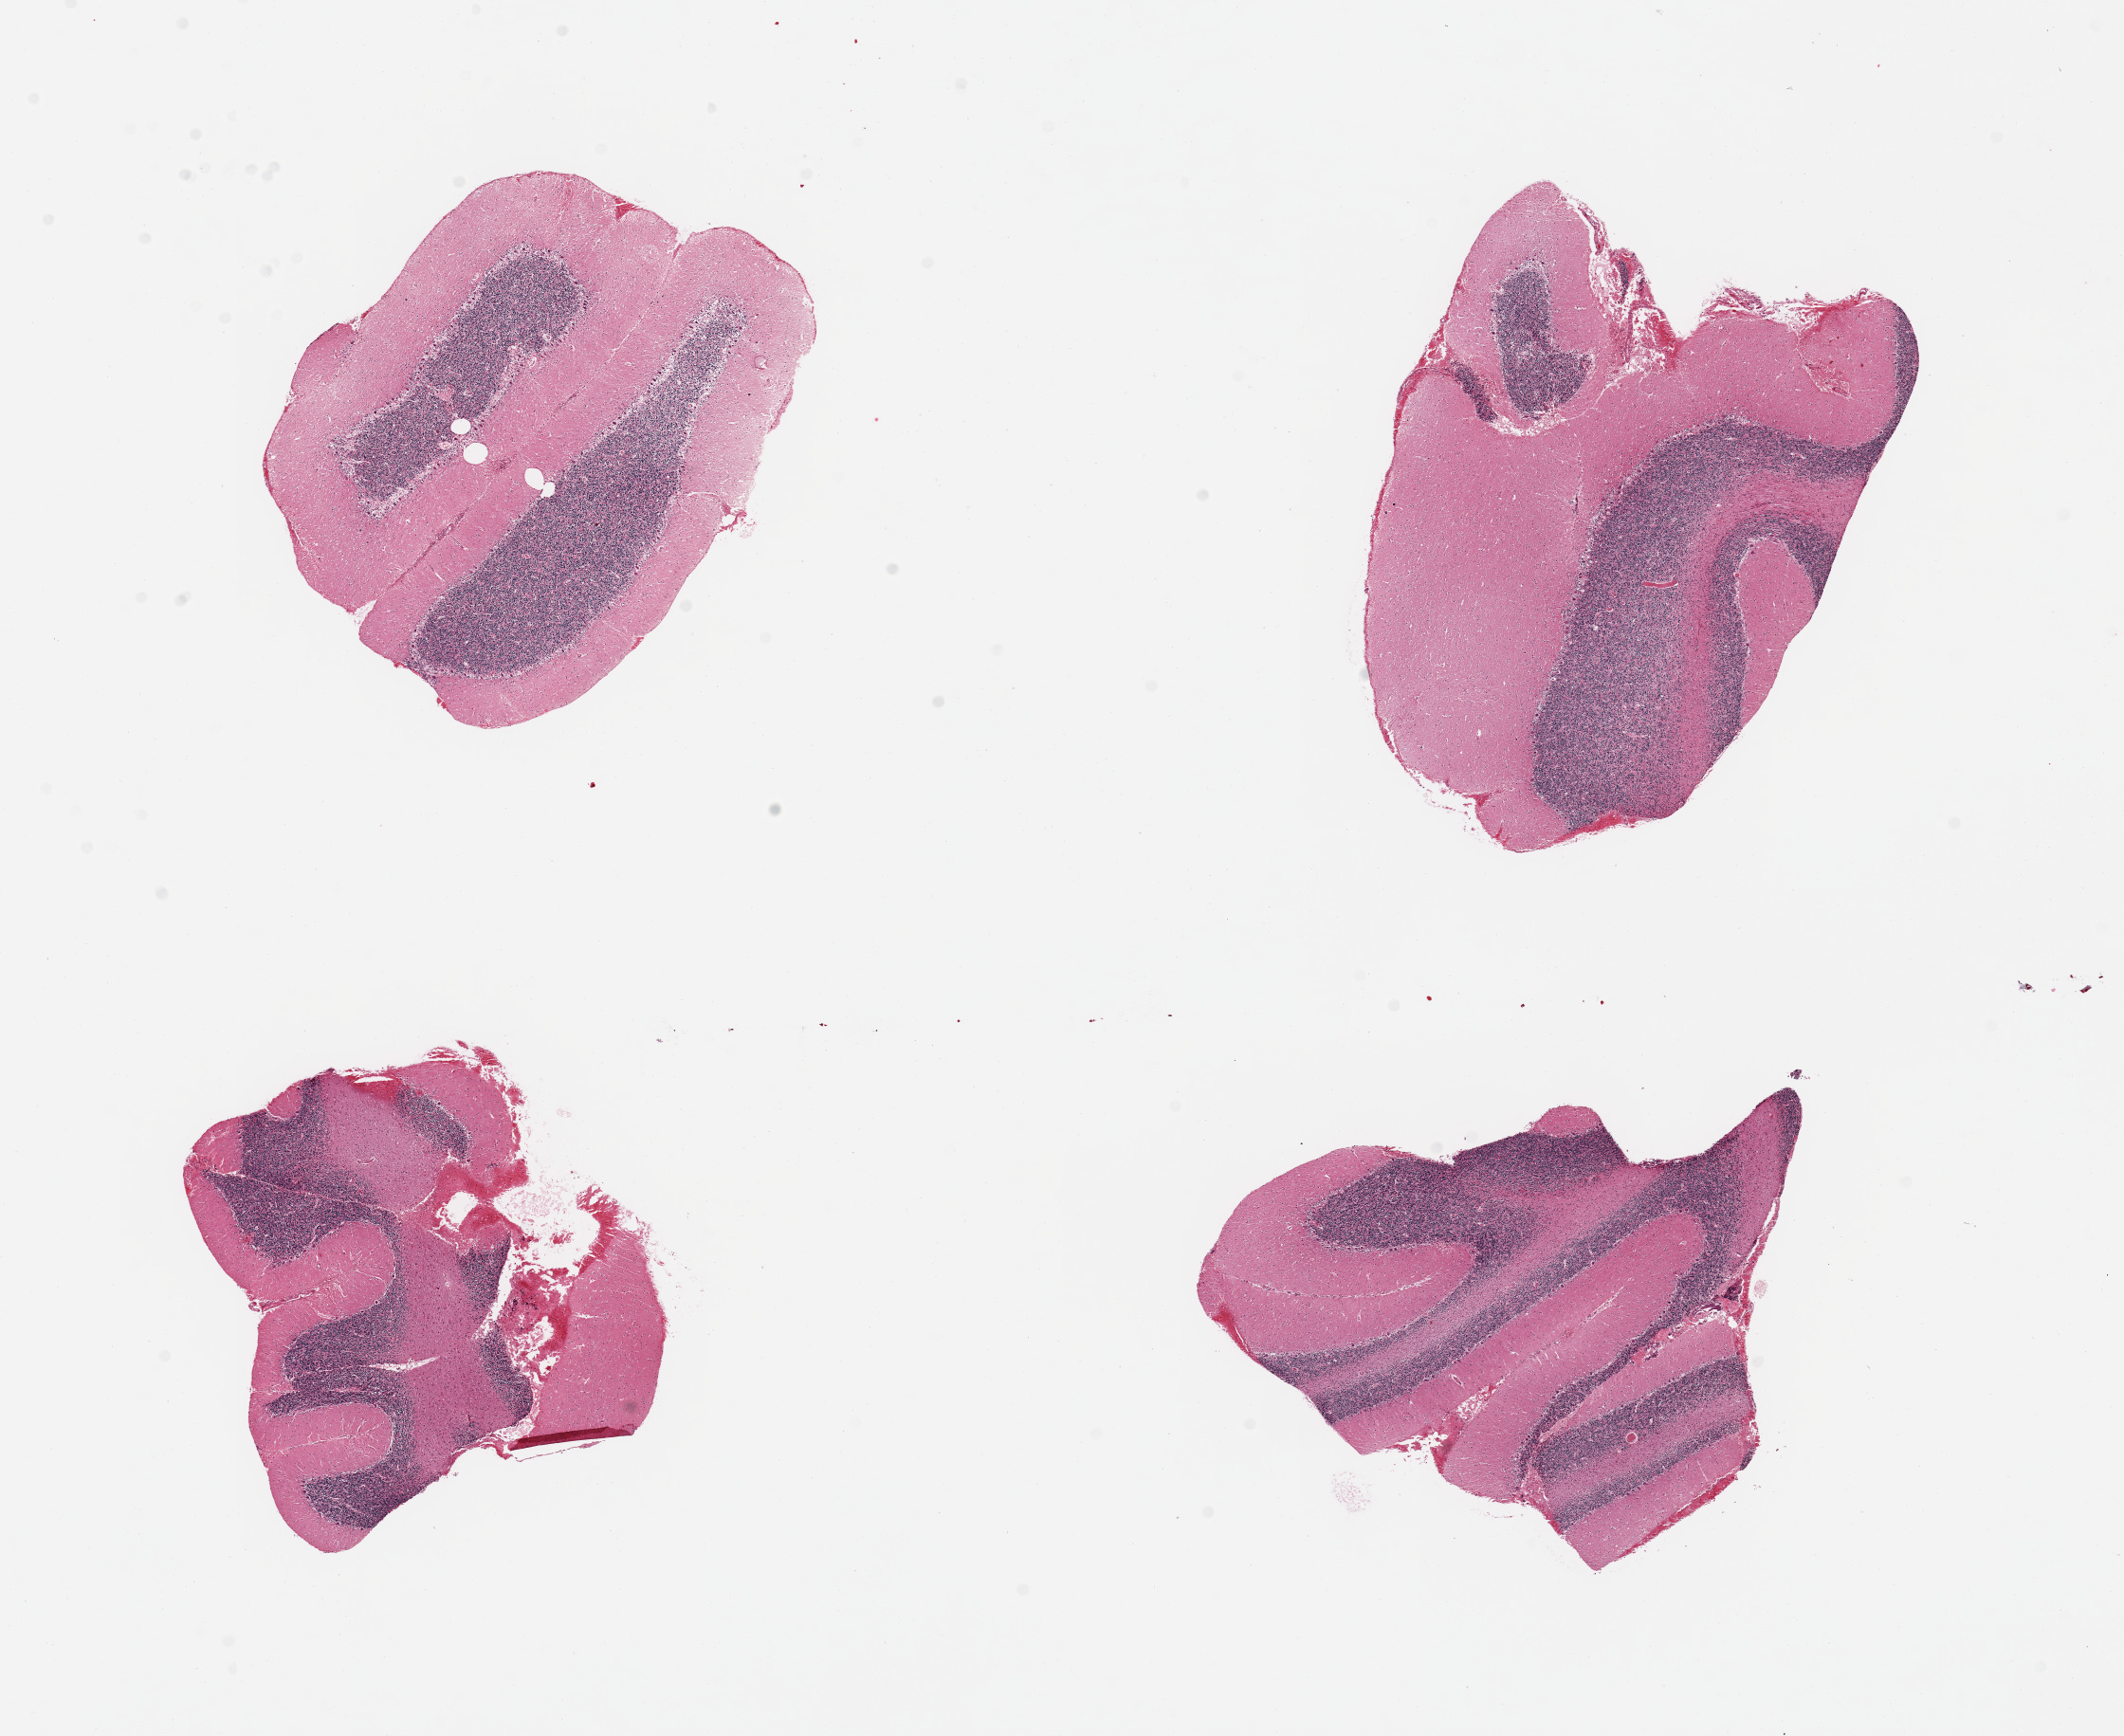
Digitized haematoxylin and eosin-stained section, low-resolution overview of the scanned area, about 17.7 x 14.5 mm; PAXgene-fixed, paraffin-embedded tissue; target tissue: cerebellum; tissue donor sample. Female donor.
* reviewer comment on this tissue sample: 4 pieces, no abnormalities